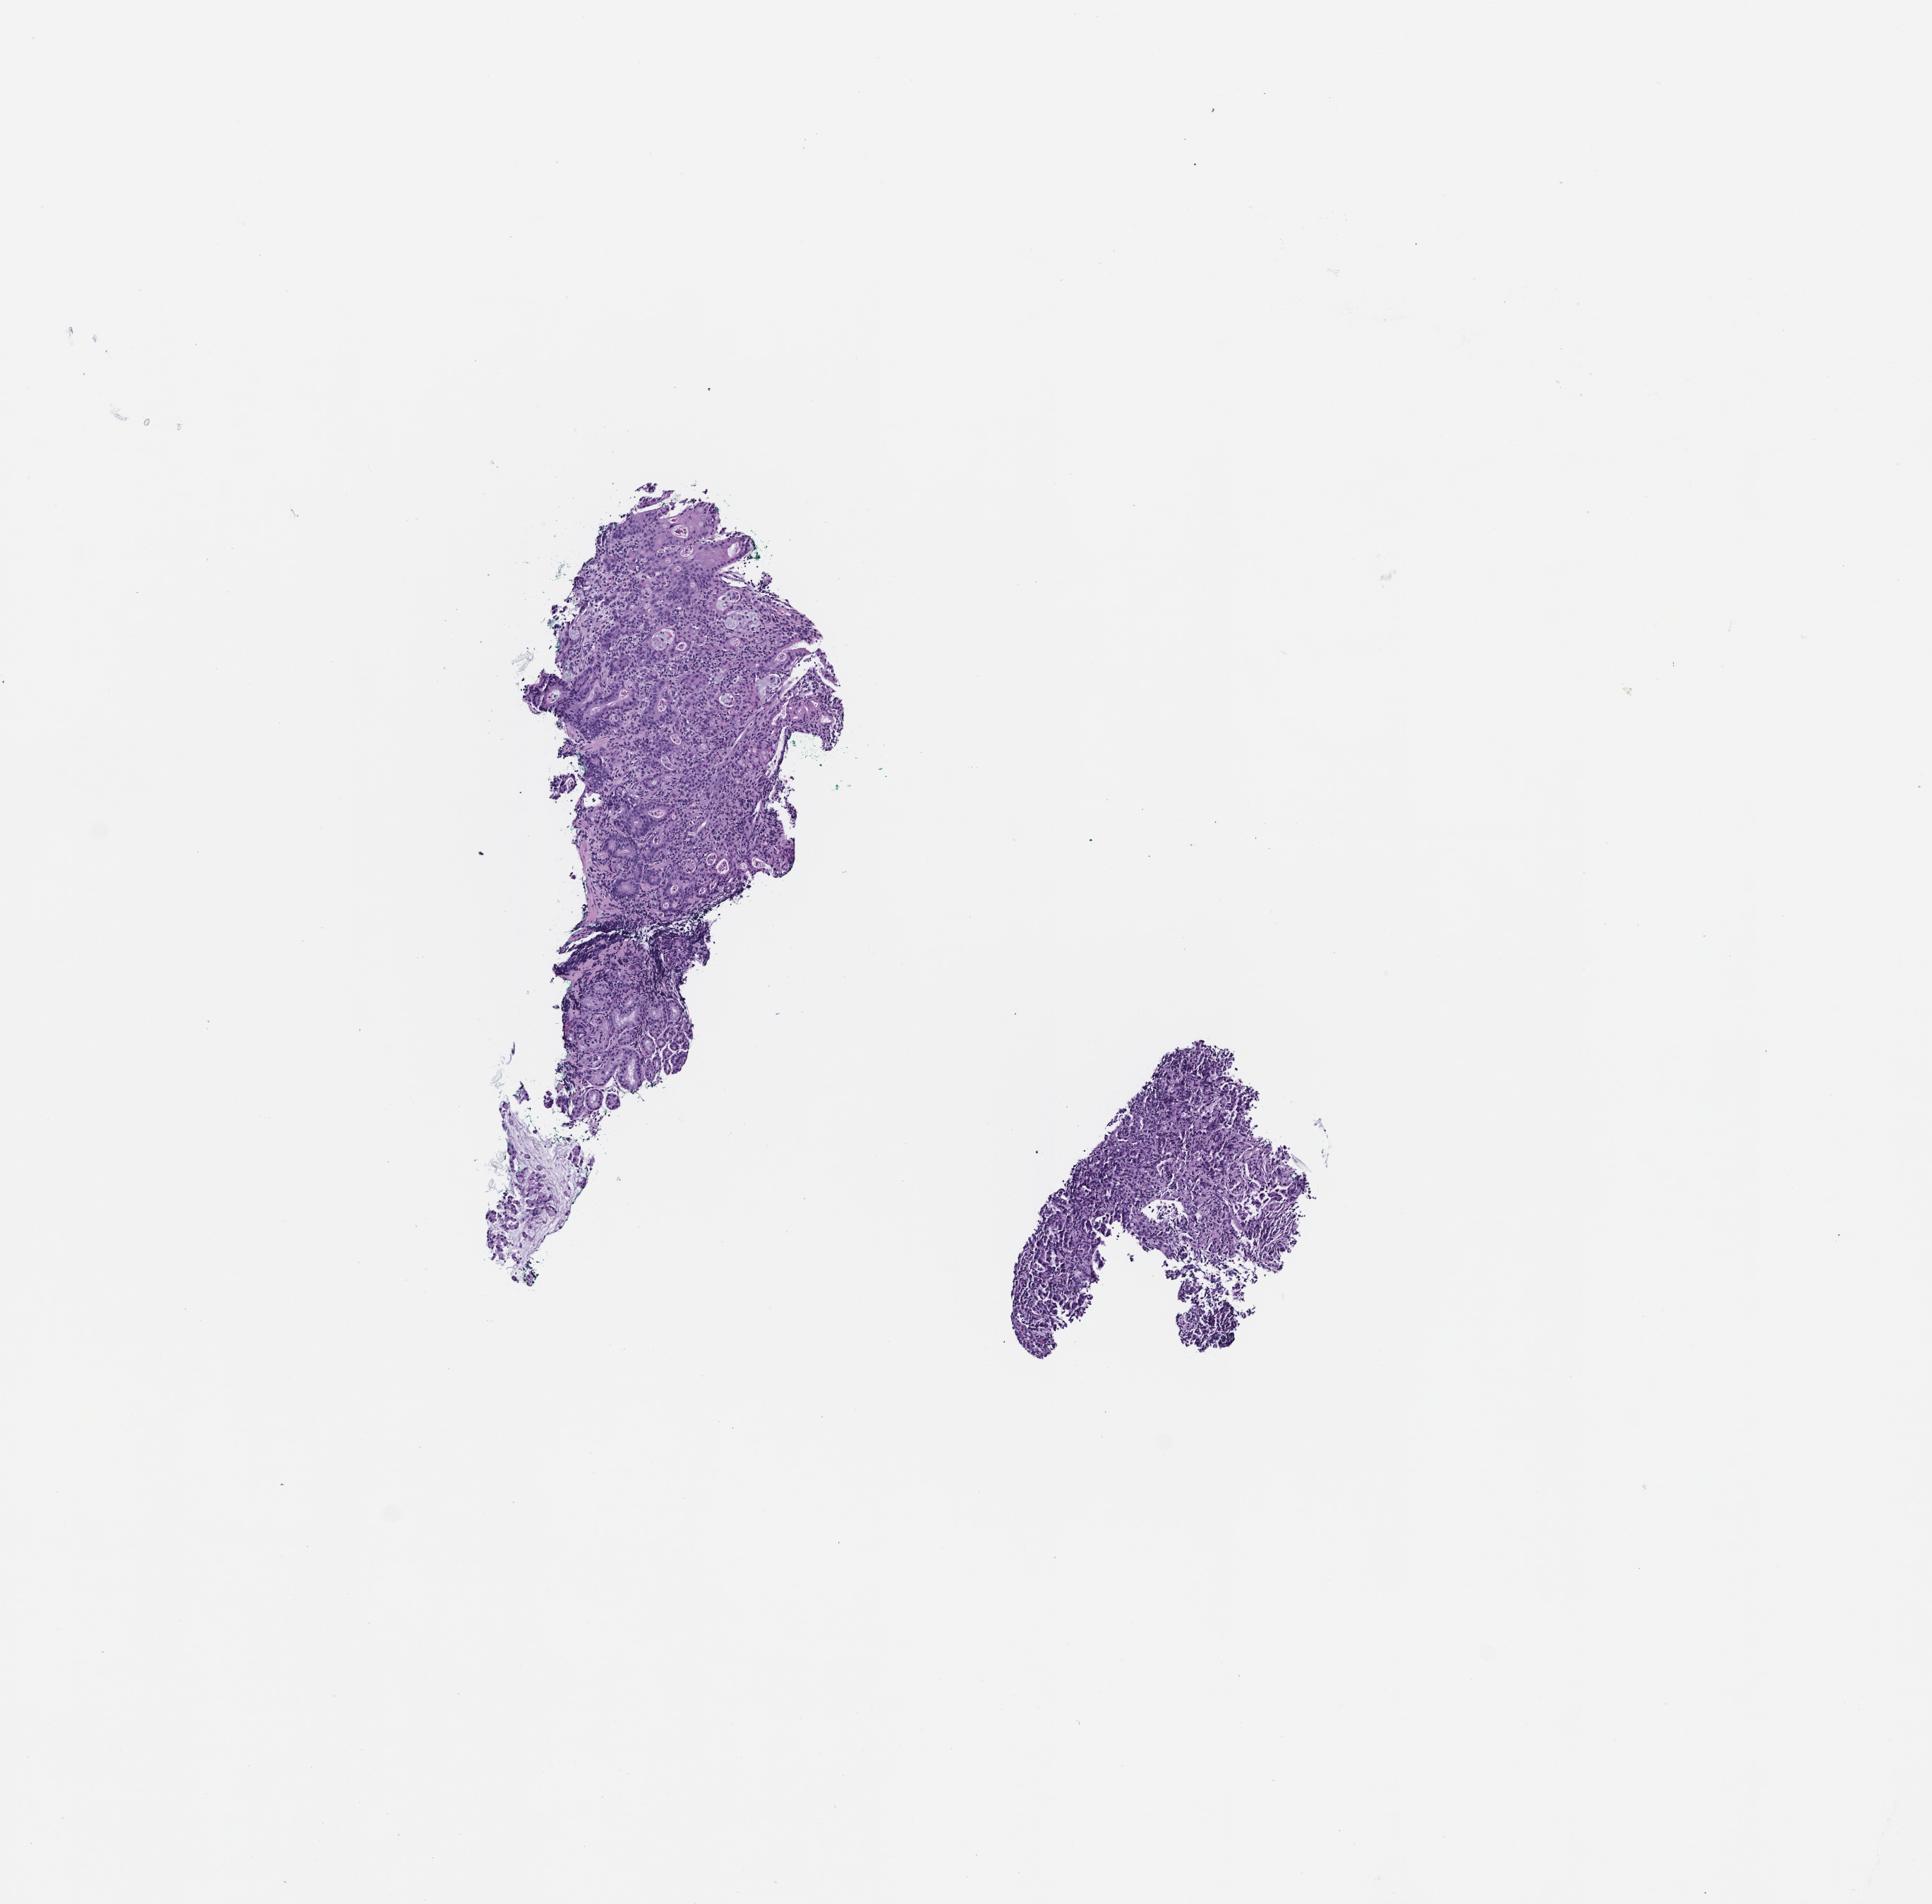
Haematoxylin and eosin whole-slide image — whole scanned area (about 5.5 x 5.4 mm) shown as a low-resolution overview. Formalin-fixed paraffin-embedded section. Tissue site: stomach. Specimen time point: archival tissue. Patient sex: male.
- this section: primary tumor
- diagnosis: Adenocarcinoma of the Gastroesophageal Junction